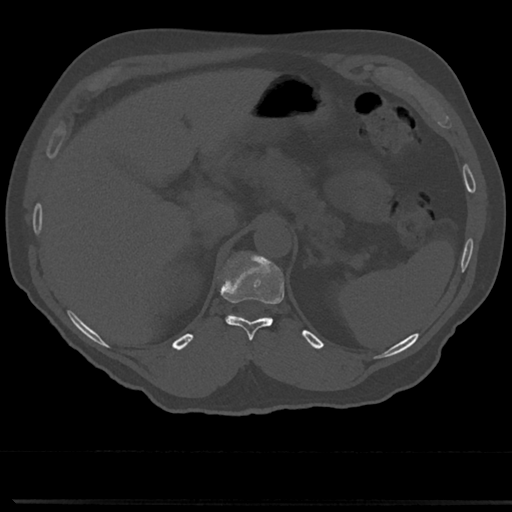
CT including the spine, one axial slice; slice 191 of 817 in the series (ordered by position); reconstruction kernel Br40s/3; 120 kVp; bone window (W 1800 / L 400 HU); 0.5 mm slice thickness; 512 × 512 image matrix, field of view 355 × 355 mm. Male patient, age 61 years. From the clinical record (not read from this slice): primary cancer: prostate.
Annotated regions visible in this slice (semi-automatic segmentation, software-assisted and operator-edited):
- T11 vertebra: bounding box (x1, y1, x2, y2) in pixels: (223, 258, 284, 342)
- T12 vertebra: (244, 255, 255, 258)